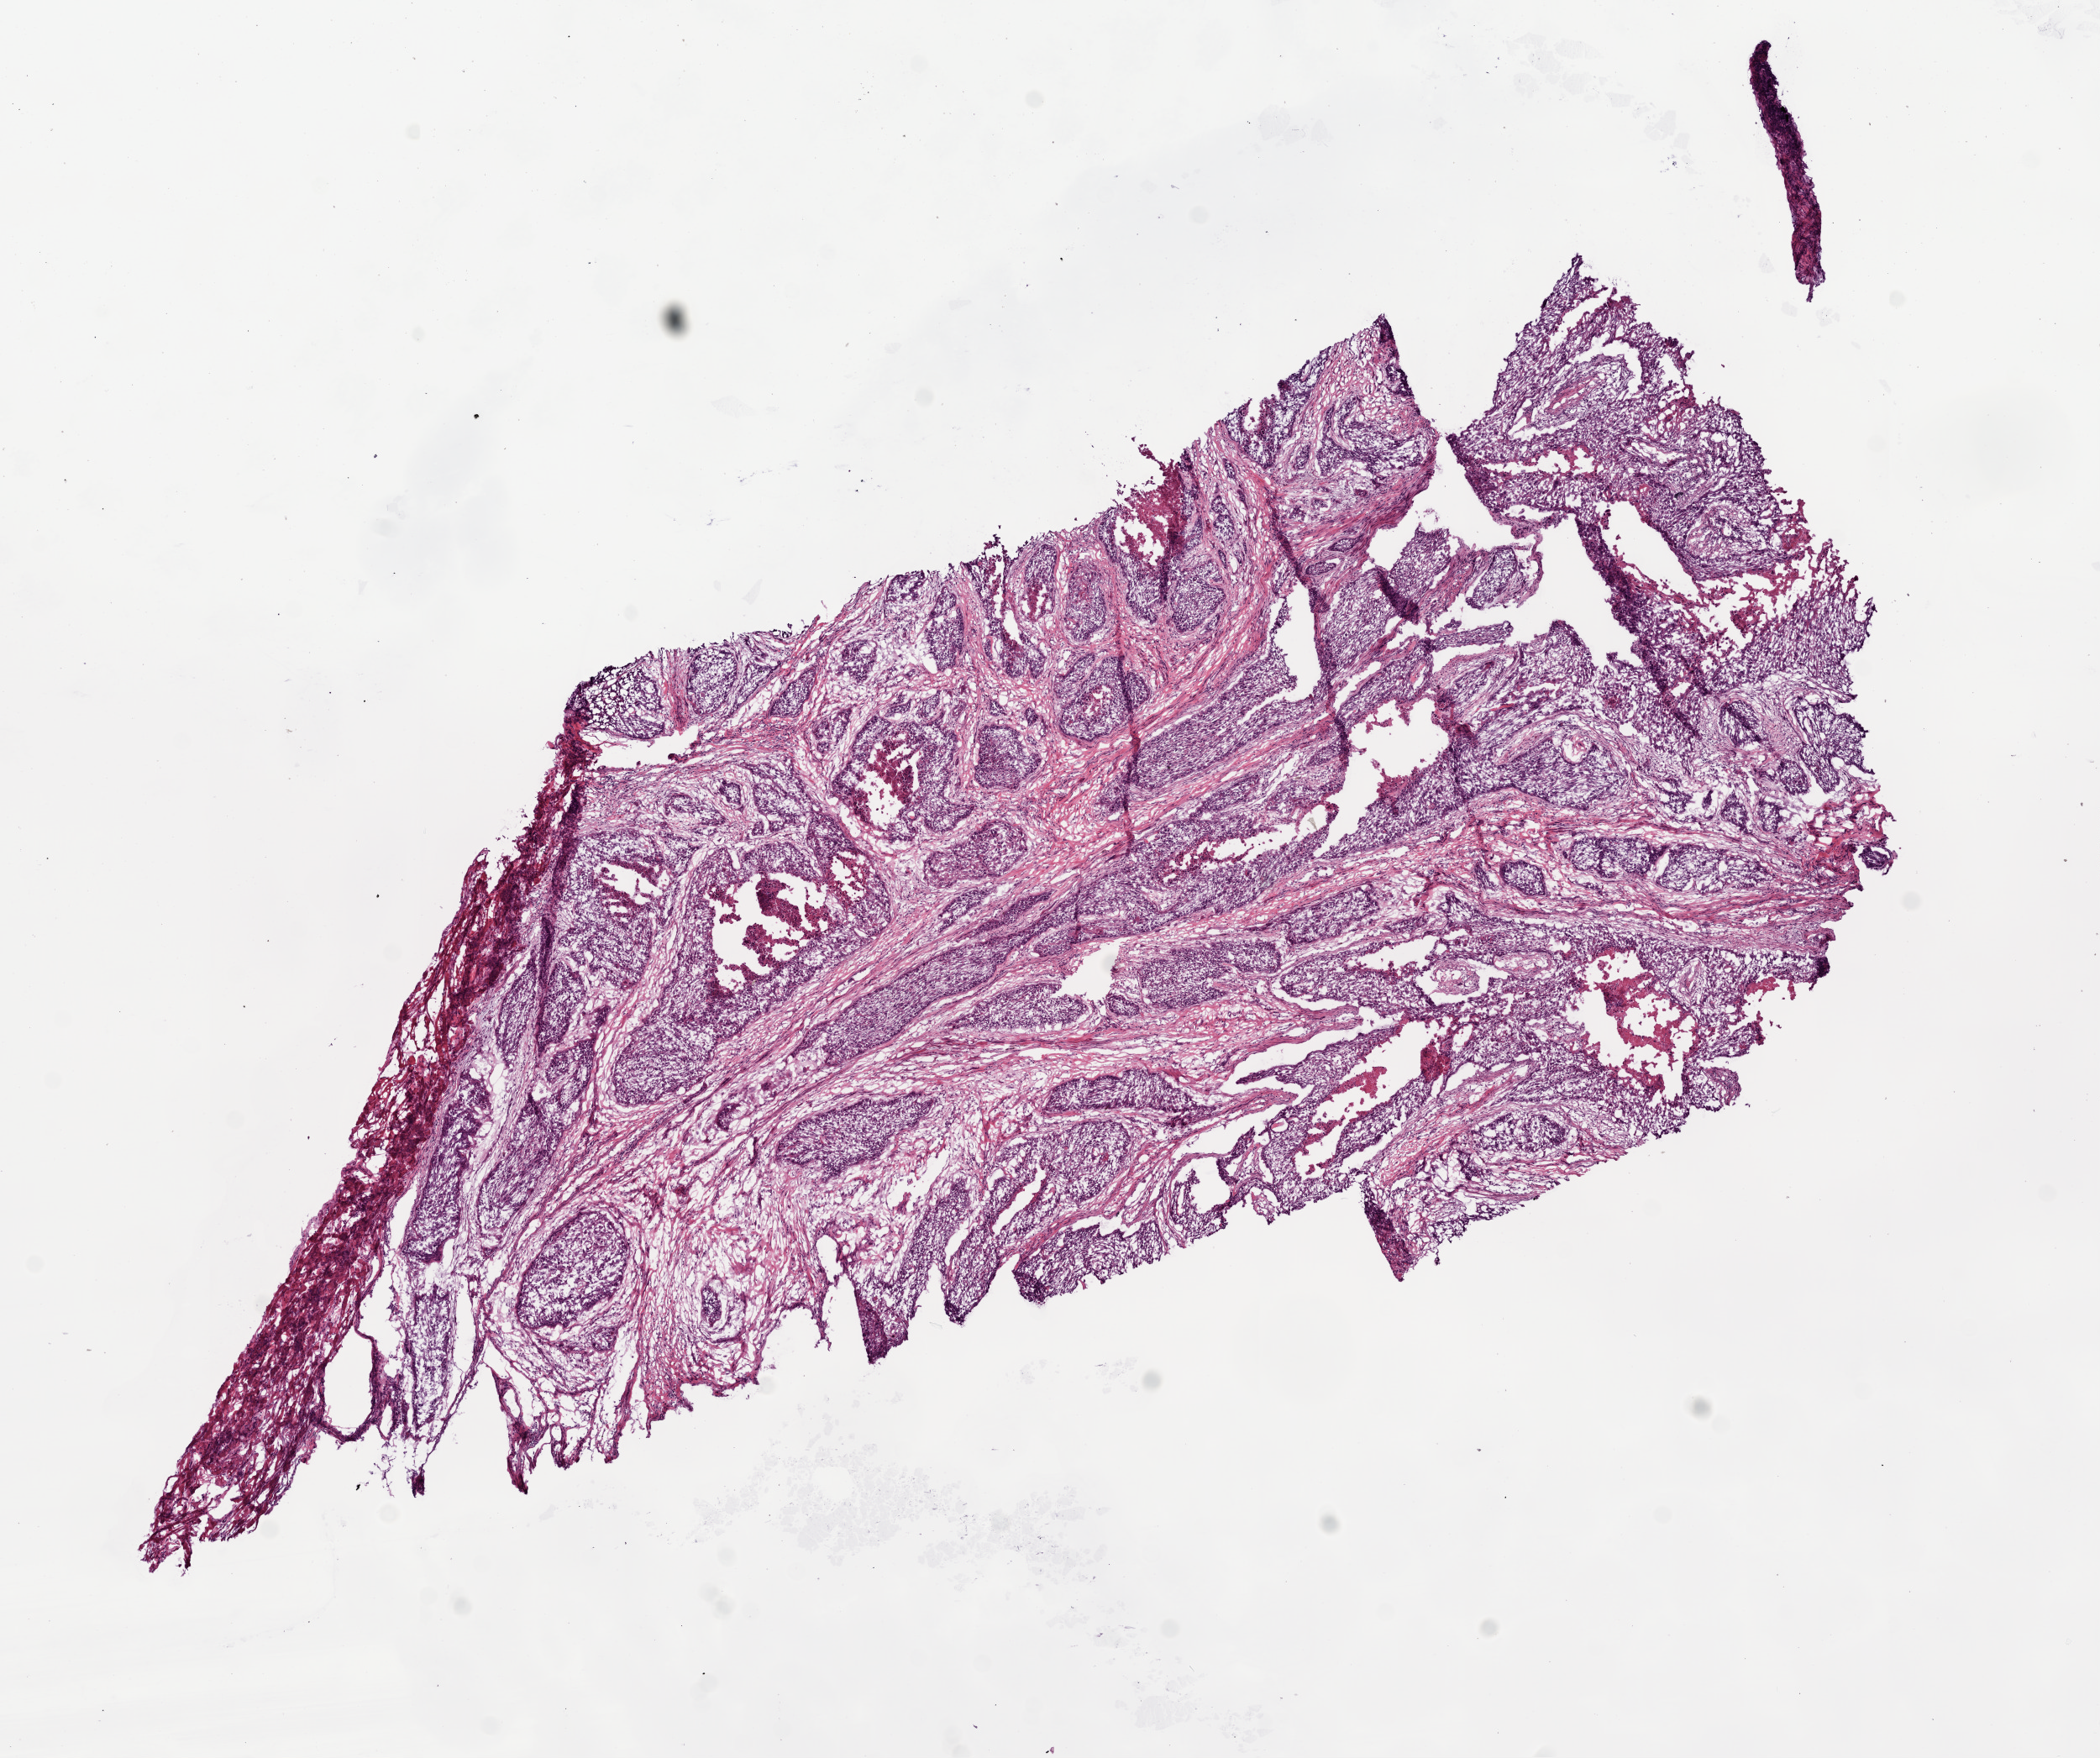
H&E whole-slide image — shown as a low-resolution overview of the whole scanned area (about 10.0 x 8.4 mm), frozen section from the bottom of the tissue portion, primary tumour sample from the head and neck. Male patient; age at initial diagnosis 57 years. Histologic grade: G3 (poorly differentiated). Slide review estimates, as recorded: tumour cells 65%, tumour nuclei 75%, normal cells 0%, stromal cells 30%, necrosis 5%.
• AJCC pathologic stage: IVA (7th edition)
• pathologic diagnosis: Squamous cell carcinoma, NOS (larynx, NOS)
• TNM: T4a N2b